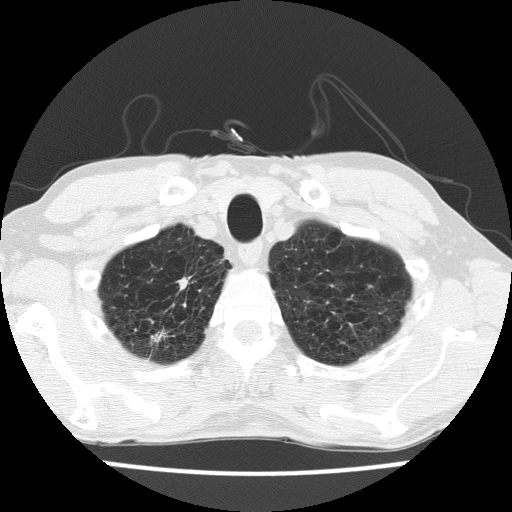
Low-dose screening chest CT, axial slice; second screening round (one year after baseline); lung window (W 1500 / L -600 HU); 512 × 512 image matrix, field of view 326 × 326 mm. Male participant, aged 63 years at enrolment.
Expert-annotated lung lesion, bounding box <136,261,203,331> (left, top, right, bottom; pixels). No non-calcified nodule or mass ≥4 mm was recorded by the screening reader at this exam. Official screen result: negative screen, minor abnormalities not suspicious for lung cancer. Later outcome: lung cancer diagnosed 390 days after this screen — adenocarcinoma, NOS, right upper lobe, moderately differentiated (G2), stage IIIB (AJCC 6th edition), 17 mm at pathology.